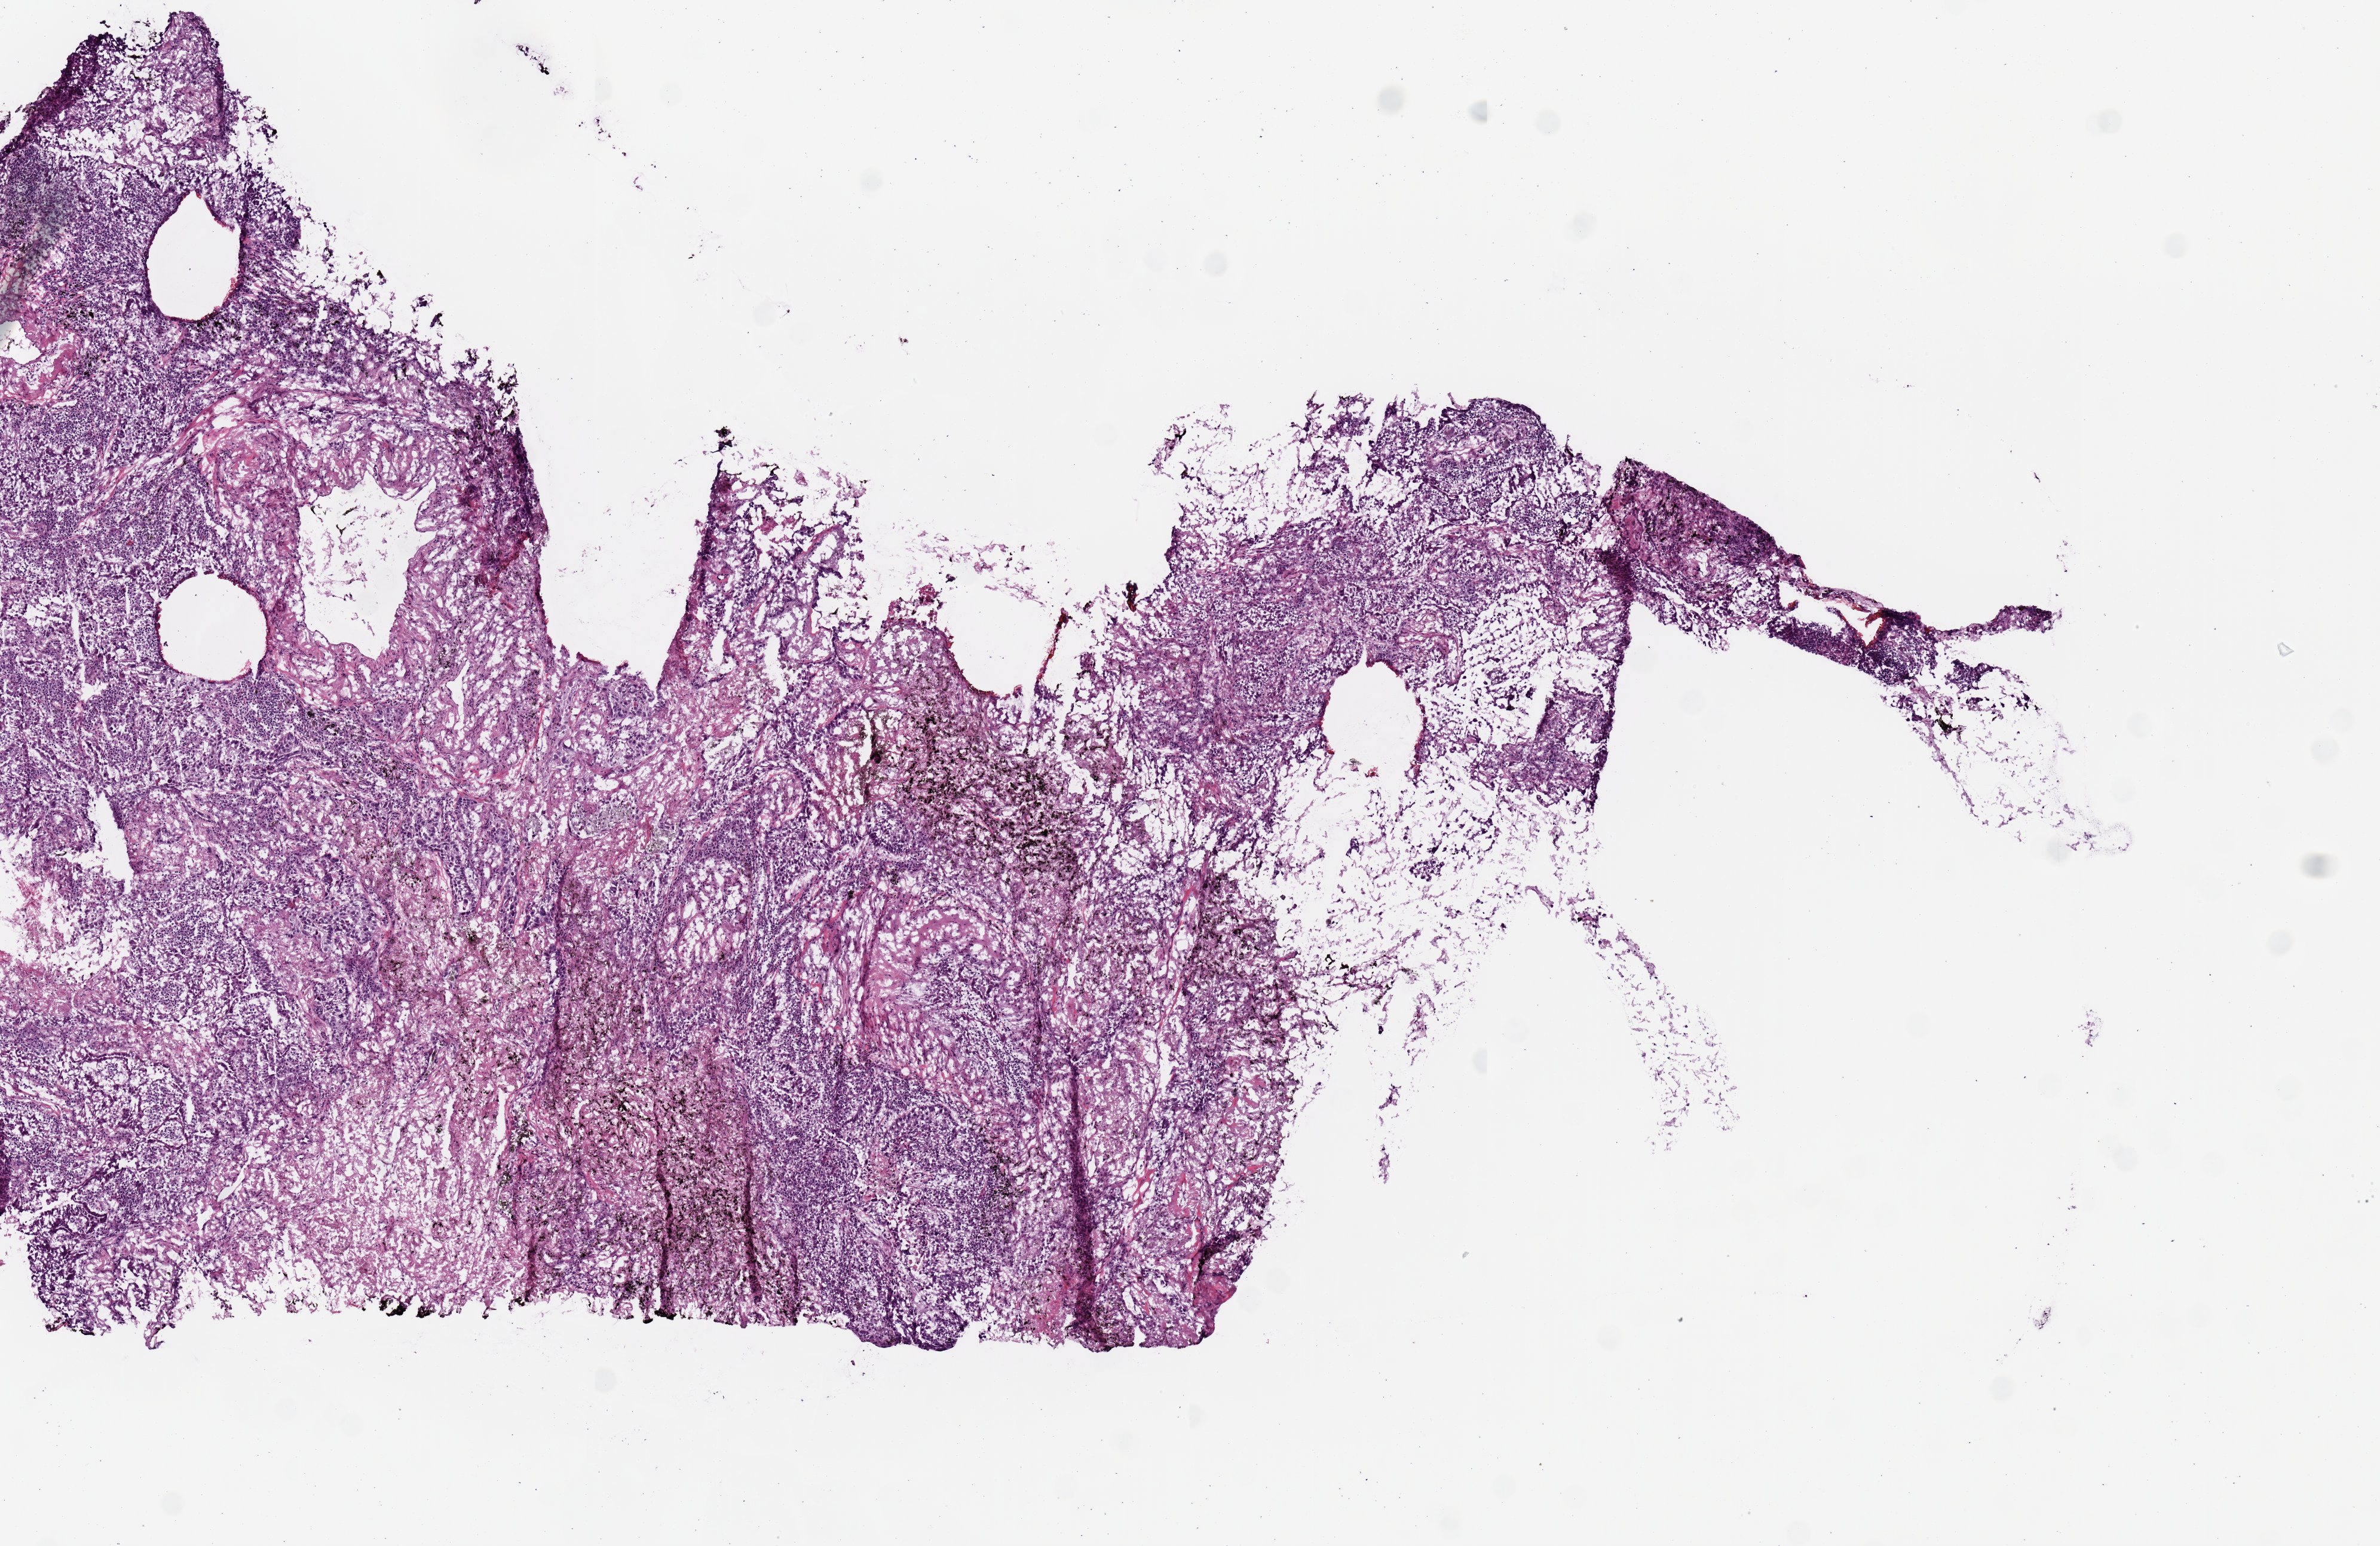
H&E-stained whole-slide image, shown as a low-resolution overview of the whole scanned area (about 7.9 x 5.1 mm), frozen section from the top of the tissue portion, lung, primary tumour sample. Patient: male, age at initial diagnosis 58 years.
Diagnosis: Adenocarcinoma, NOS (lower lobe, lung).